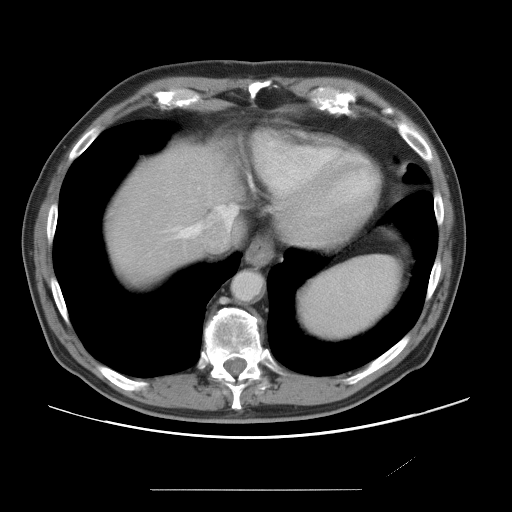
Contrast-enhanced abdominal CT, one axial slice. Position 66 of 87 along the scan axis. 120 kVp. Intravenous contrast given. Soft-tissue window (W 400 / L 40 HU). 5 mm slice thickness. 512 × 512 image matrix, field of view 406 × 406 mm. Male patient, age 74 years. Case-level facts recorded for this patient, not image findings: diagnosis: colorectal cancer liver metastases, imaged before liver resection; multiple liver metastases: yes; largest metastasis: 1.1 cm; chemotherapy before resection: yes.
Annotated regions visible in this slice (outlined manually by an expert reader):
- hepatic veins: box from (x=173, y=205) to (x=223, y=238) px
- liver: (x=110, y=149)–(x=237, y=284)
- planned liver remnant (the part of the liver to remain after resection): (x=111, y=148)–(x=237, y=283)